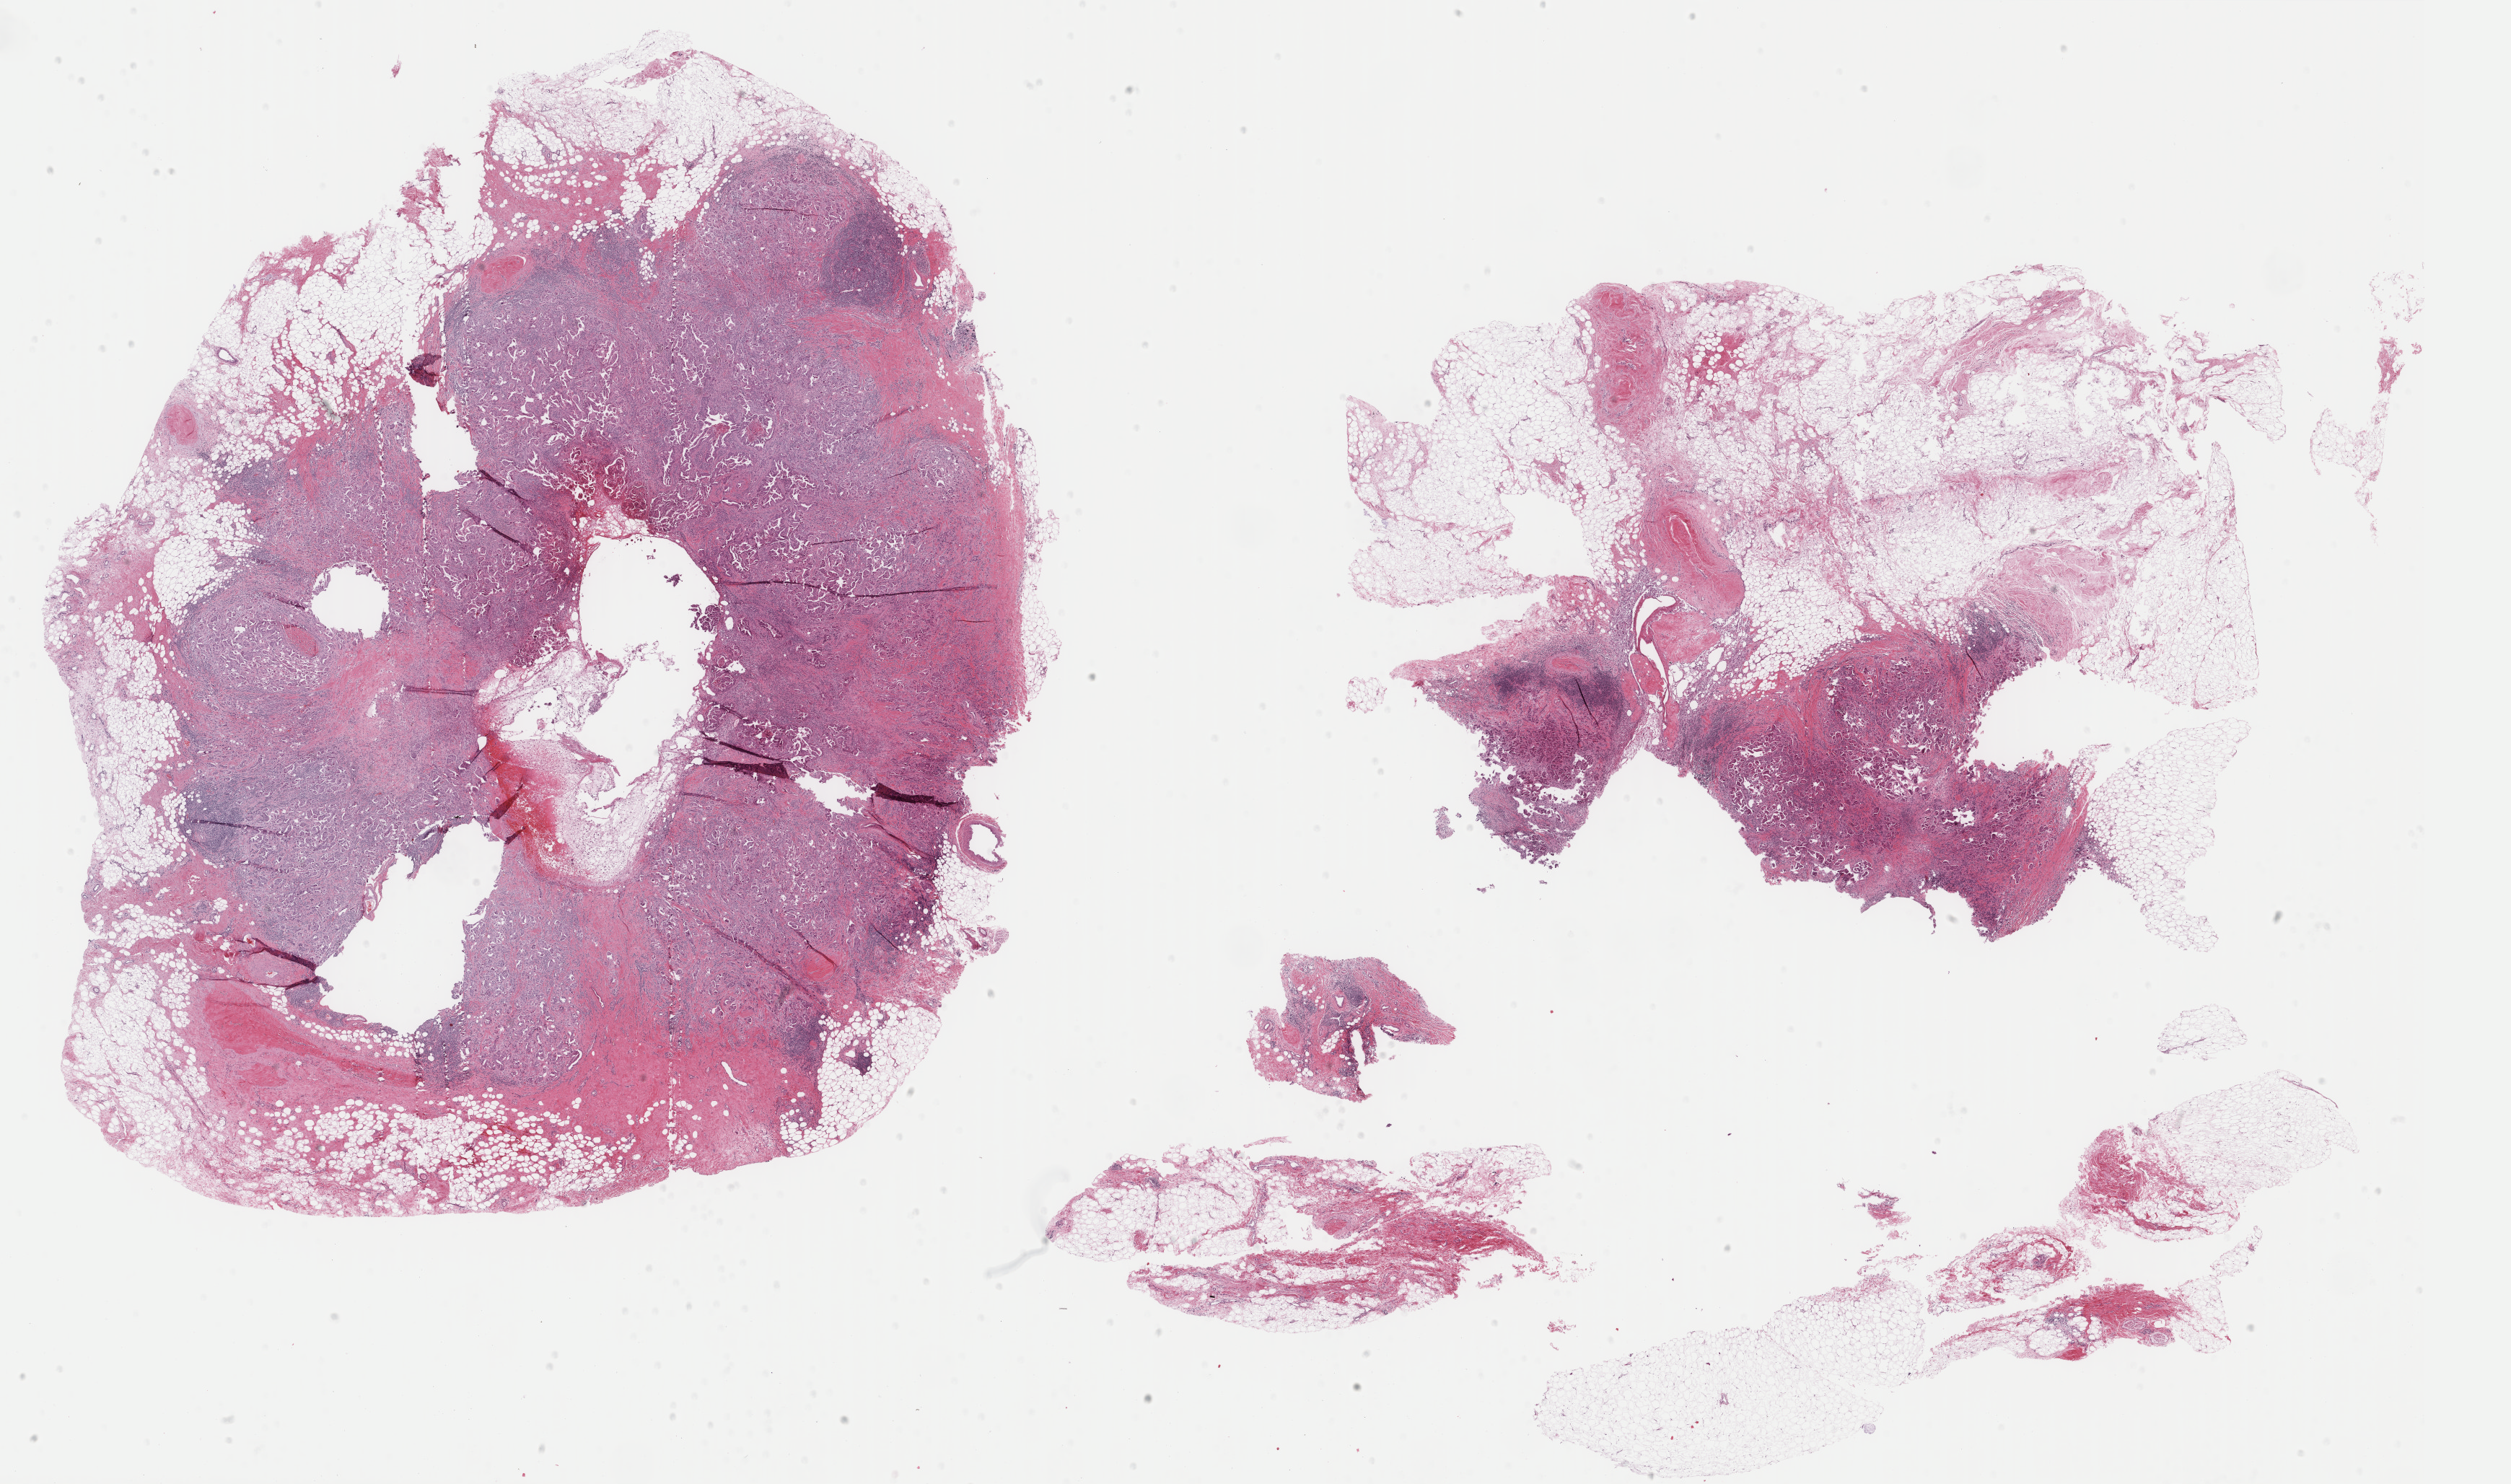
H&E whole-slide image, low-resolution overview of the scanned area, about 27.6 x 16.3 mm. Formalin-fixed paraffin-embedded (FFPE) diagnostic section. Primary tumour sample from the breast. Female patient; age at initial diagnosis 47 years.
Lymph nodes positive (case pathology): 2 of 25 examined. AJCC pathologic stage: IIA (6th edition). Pathologic diagnosis: Infiltrating duct carcinoma, NOS.